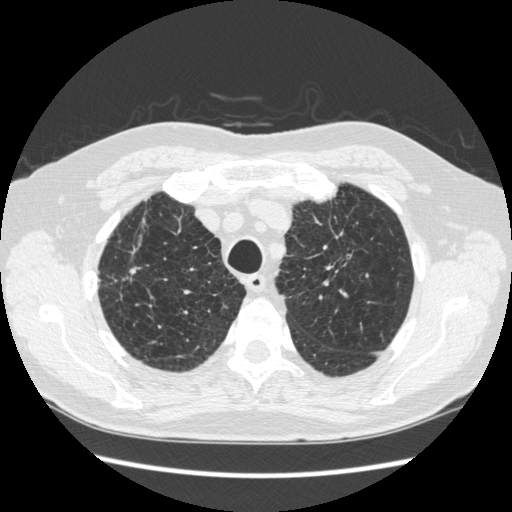
Chest CT (low-dose screening protocol), one axial image, third annual screen, lung window (W 1500 / L -600 HU), 1.25 mm slice thickness, standard (soft-tissue) reconstruction kernel (STANDARD), slice 52 of 267 in the series, 512 × 512 image matrix, field of view 360 × 360 mm. Male participant, aged 70 years at enrolment.
• Expert-annotated lung lesion, bounding box (x1, y1, x2, y2) in pixels: (322, 210, 371, 275).
• The screening reader recorded 2 non-calcified nodules or masses ≥4 mm on this exam; which of them this box marks is not recorded.
• Participant outcome: lung cancer diagnosed 92 days after this screen — squamous cell carcinoma, NOS, left upper lobe, moderately differentiated (G2), stage IA (AJCC 6th edition), 18 mm at pathology.